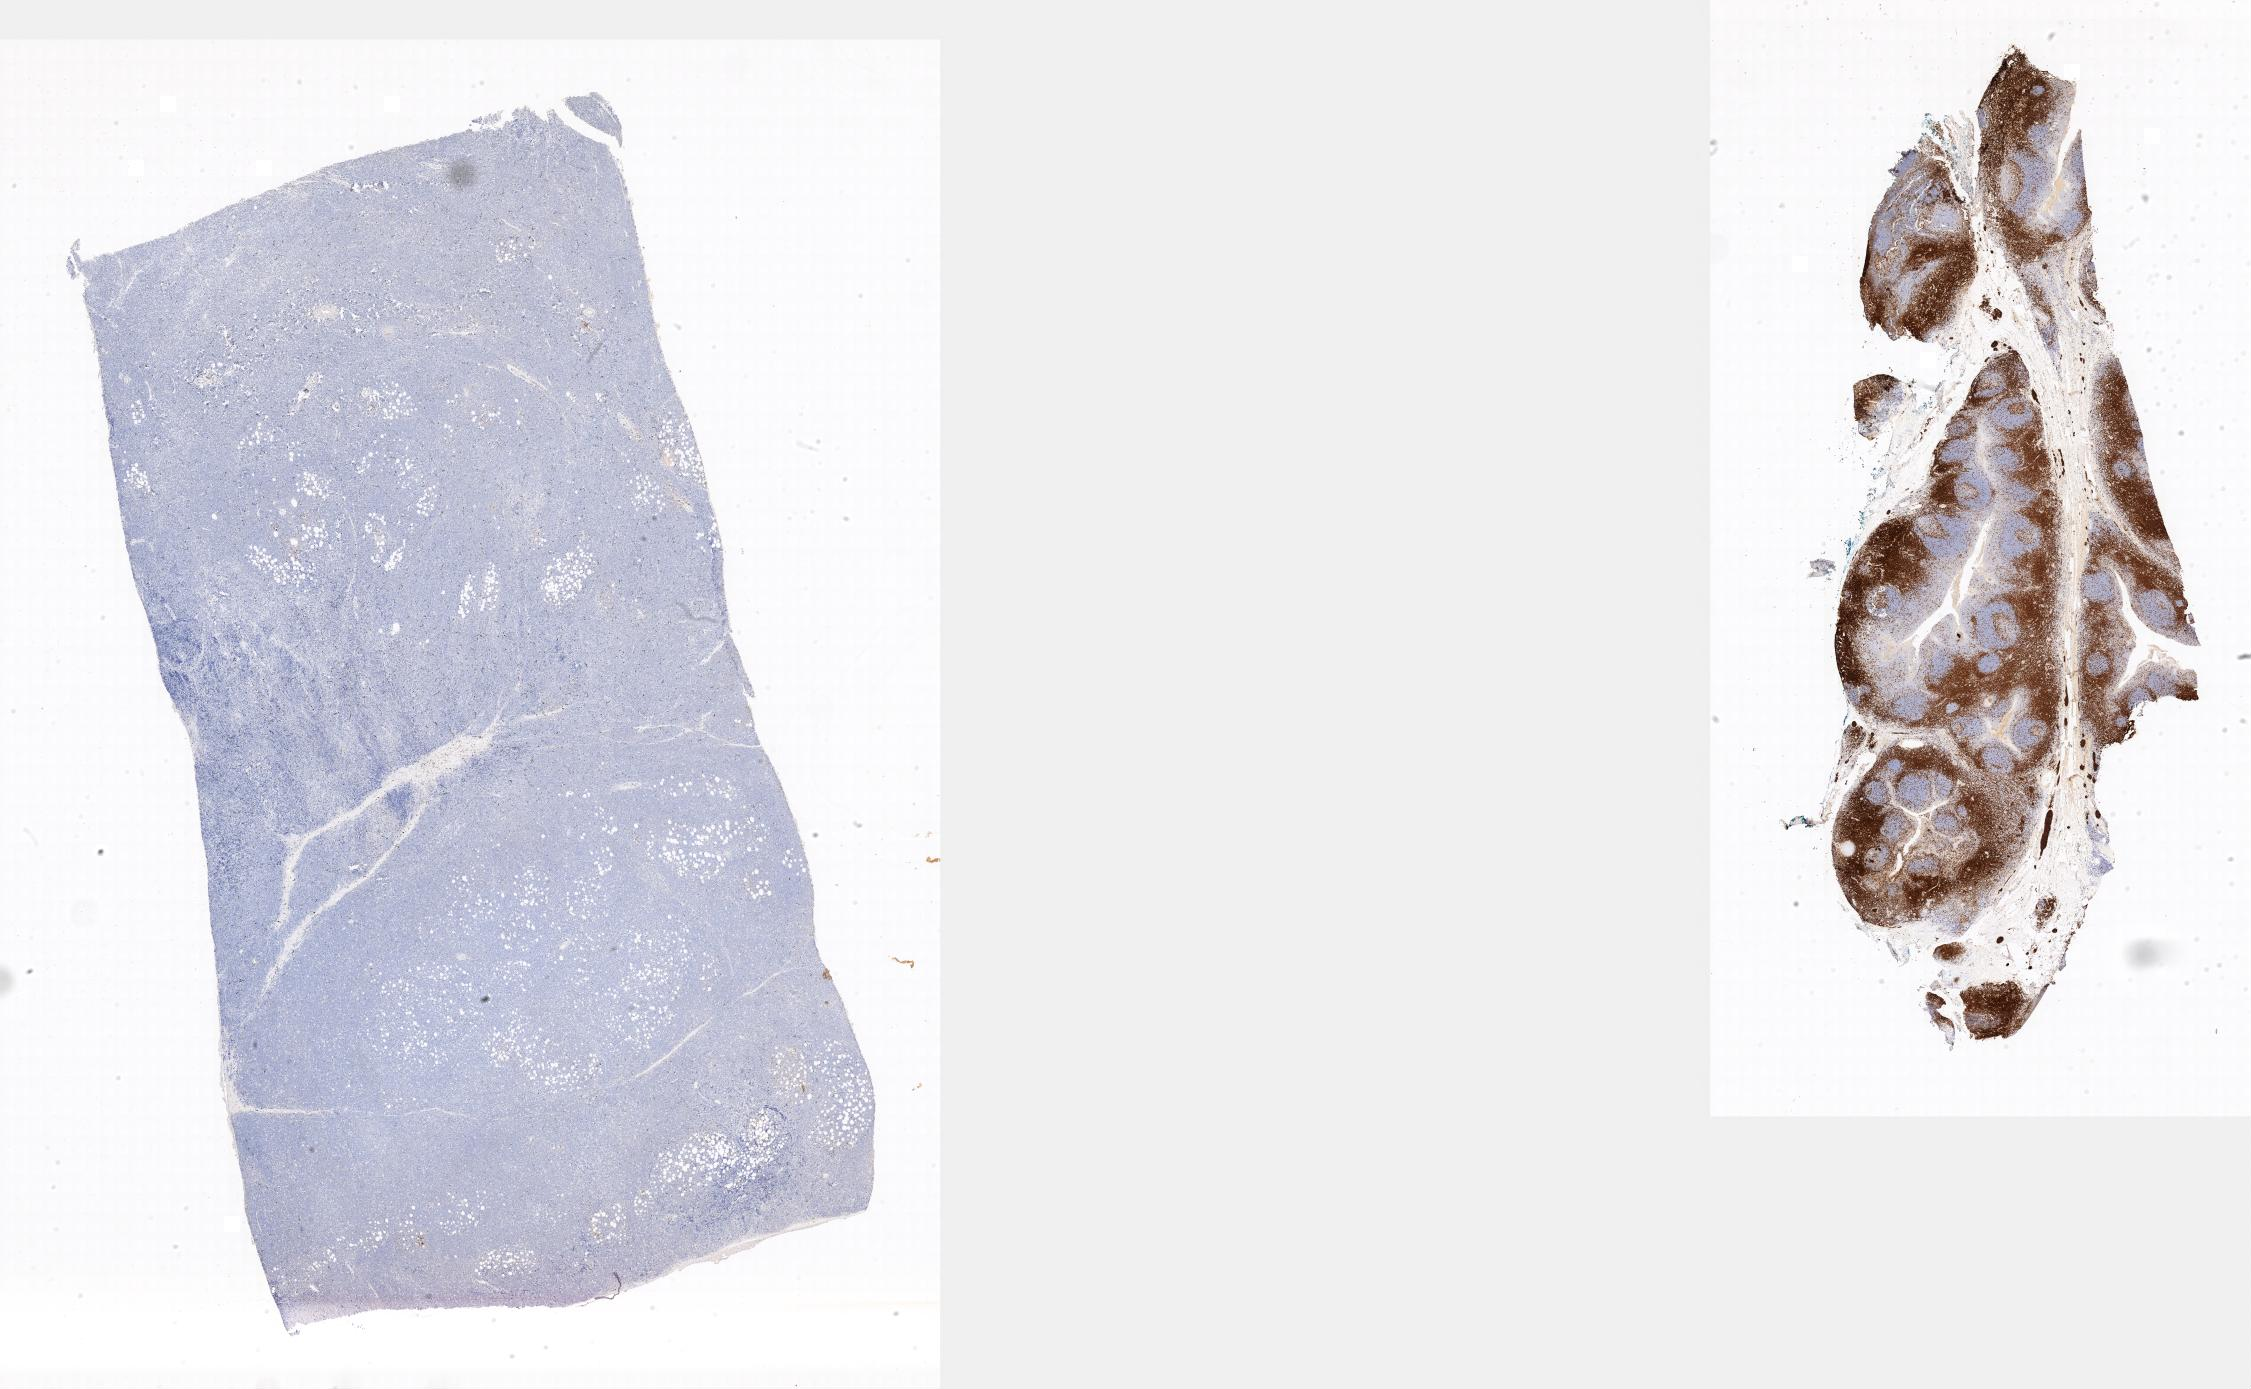
Whole-slide image, immunohistochemical stain for CD3 — low-resolution overview of the scanned area. Tumor tissue. Anatomic site: colon. Patient female; age 12 years.
Histologic diagnosis: Burkitt lymphoma, NOS.